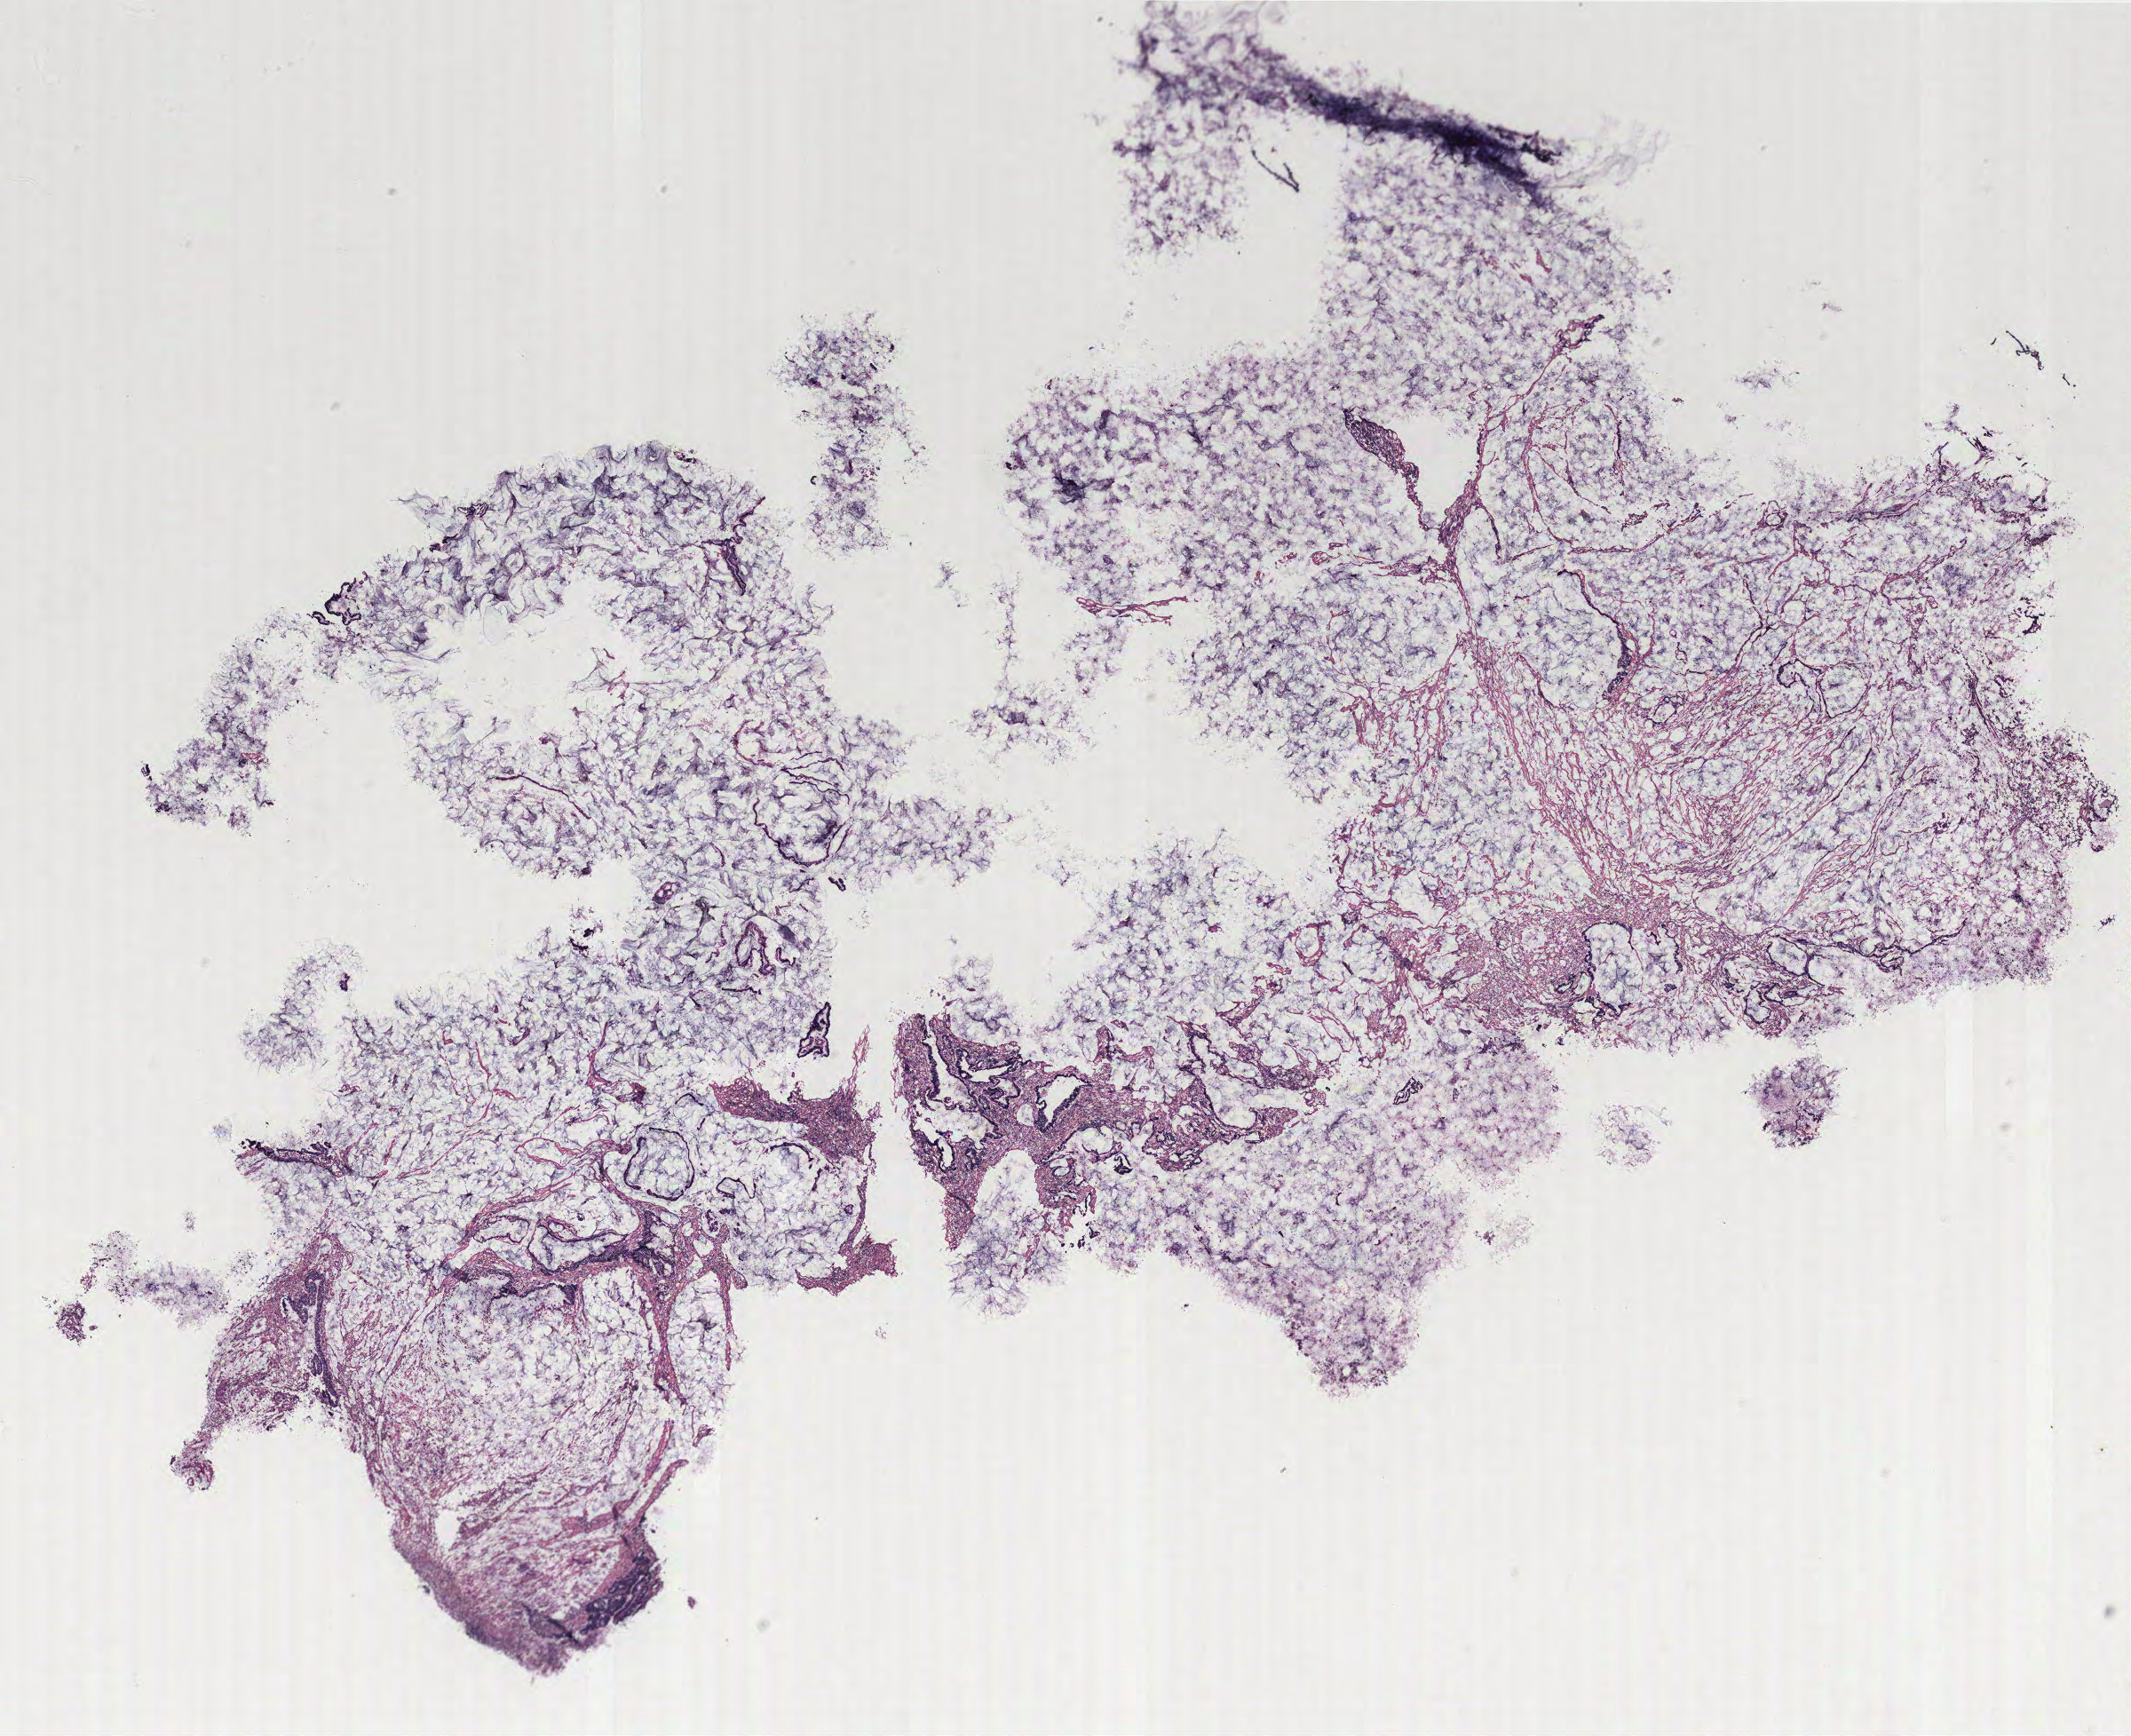
Digitized Hematoxylin and eosin (H&E) stained tissue section (whole slide) — whole scanned area (about 19.2 x 15.6 mm, slide scanned at 40x) shown as a low-resolution overview, colon, tissue type not recorded.
* patient diagnosis (cohort enrolment): colon cancer (colon)